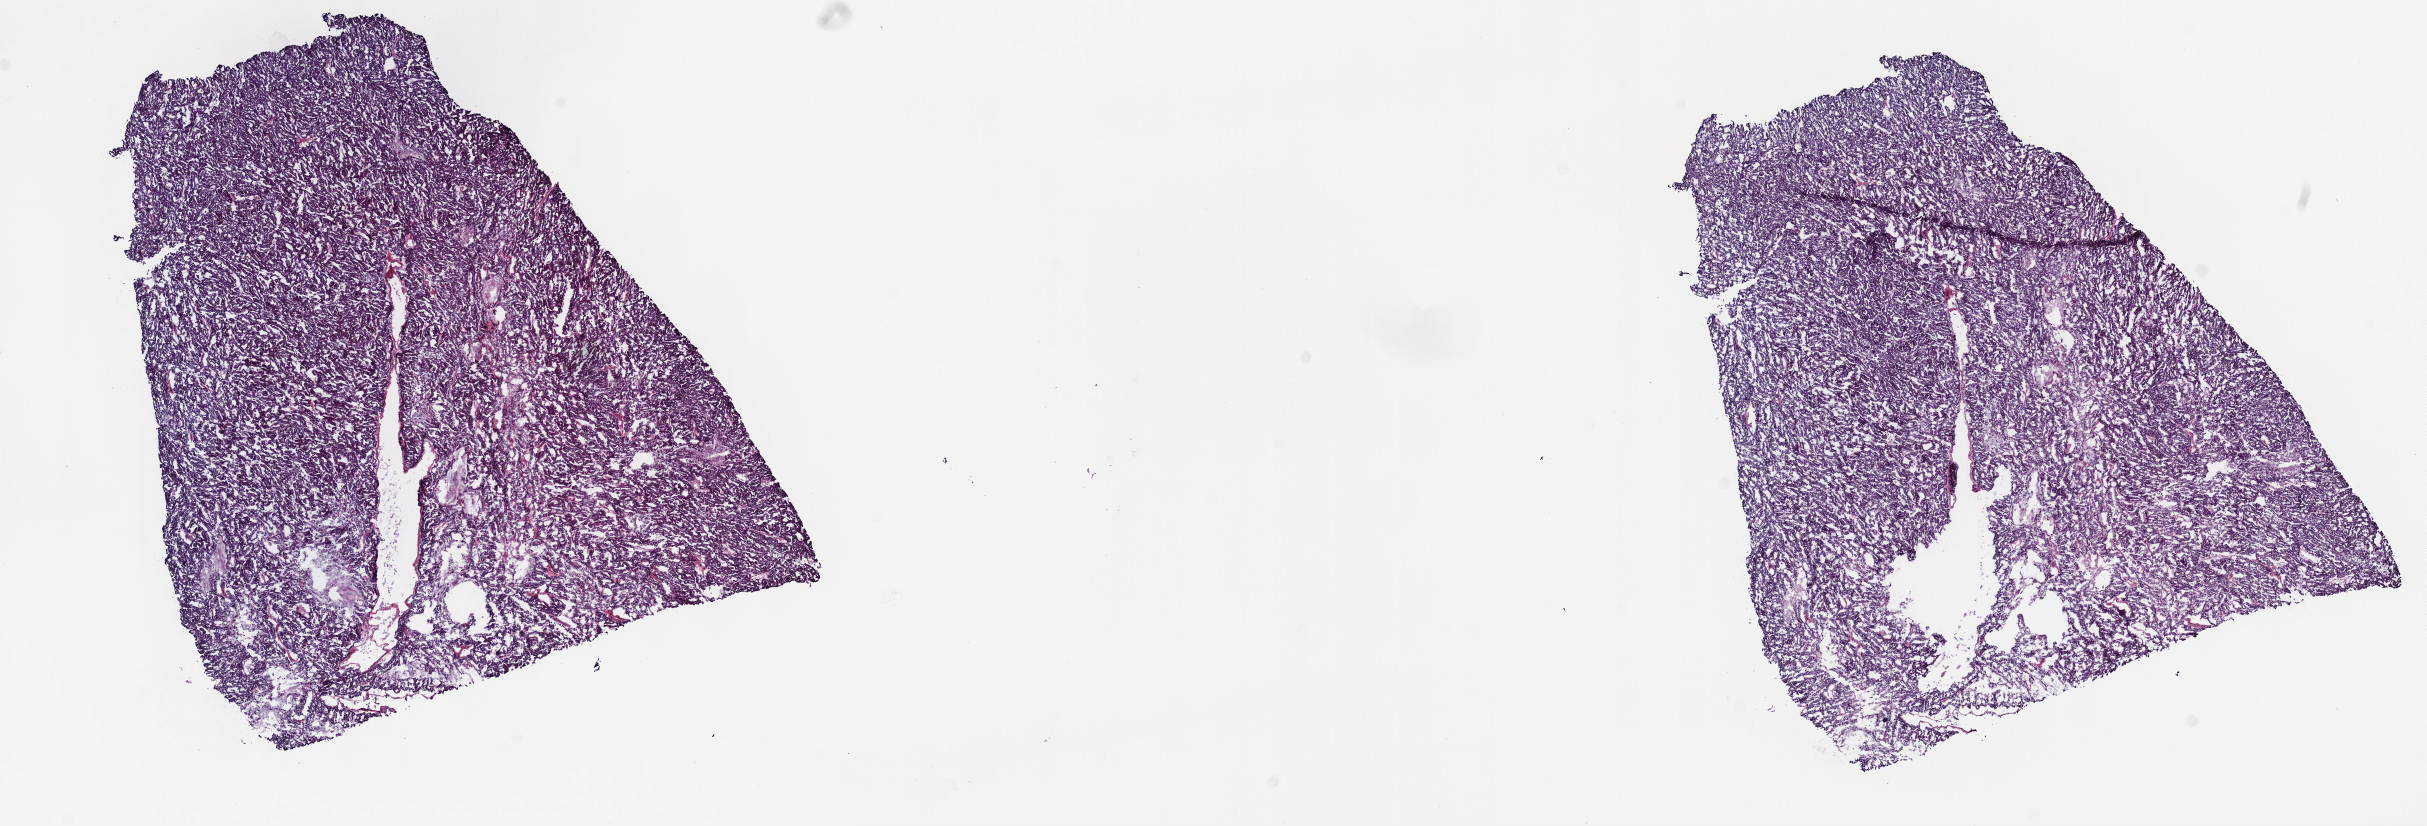
H&E whole-slide image, shown as a low-resolution overview of the whole scanned area (about 19.6 x 6.7 mm, acquisition: 40x scan). Frozen section. Kidney, primary tumour sample. Male, age 63 years at initial diagnosis. Pathologist review of this section (percent, as recorded): tumour cells 95%, tumour nuclei 95%, normal cells 0%, stromal cells 3%, necrosis 2%. Infiltration values recorded for this section: lymphocyte infiltration 2%, monocyte infiltration 2%, neutrophil infiltration 0%.
Diagnosis: Papillary adenocarcinoma, NOS. AJCC pathologic stage: IV (6th edition).